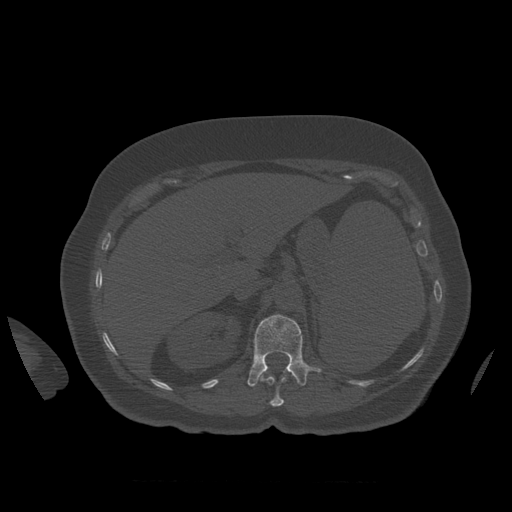
CT including the spine, one axial slice. Slice 285 of 399 in the series (ordered by position). Reconstruction kernel STANDARD. 120 kVp. Bone window (W 1800 / L 400 HU). 1.25 mm slice thickness. 512 × 512 image matrix. Patient age 81 years. Case-level facts recorded for this patient, not image findings: primary cancer: renal.
Structures marked on this image (semi-automatic segmentation, software-assisted and operator-edited):
- L1 vertebra: bounding box (x1, y1, x2, y2) in pixels: (247, 315, 322, 387)
- T12 vertebra: (261, 372, 293, 407)